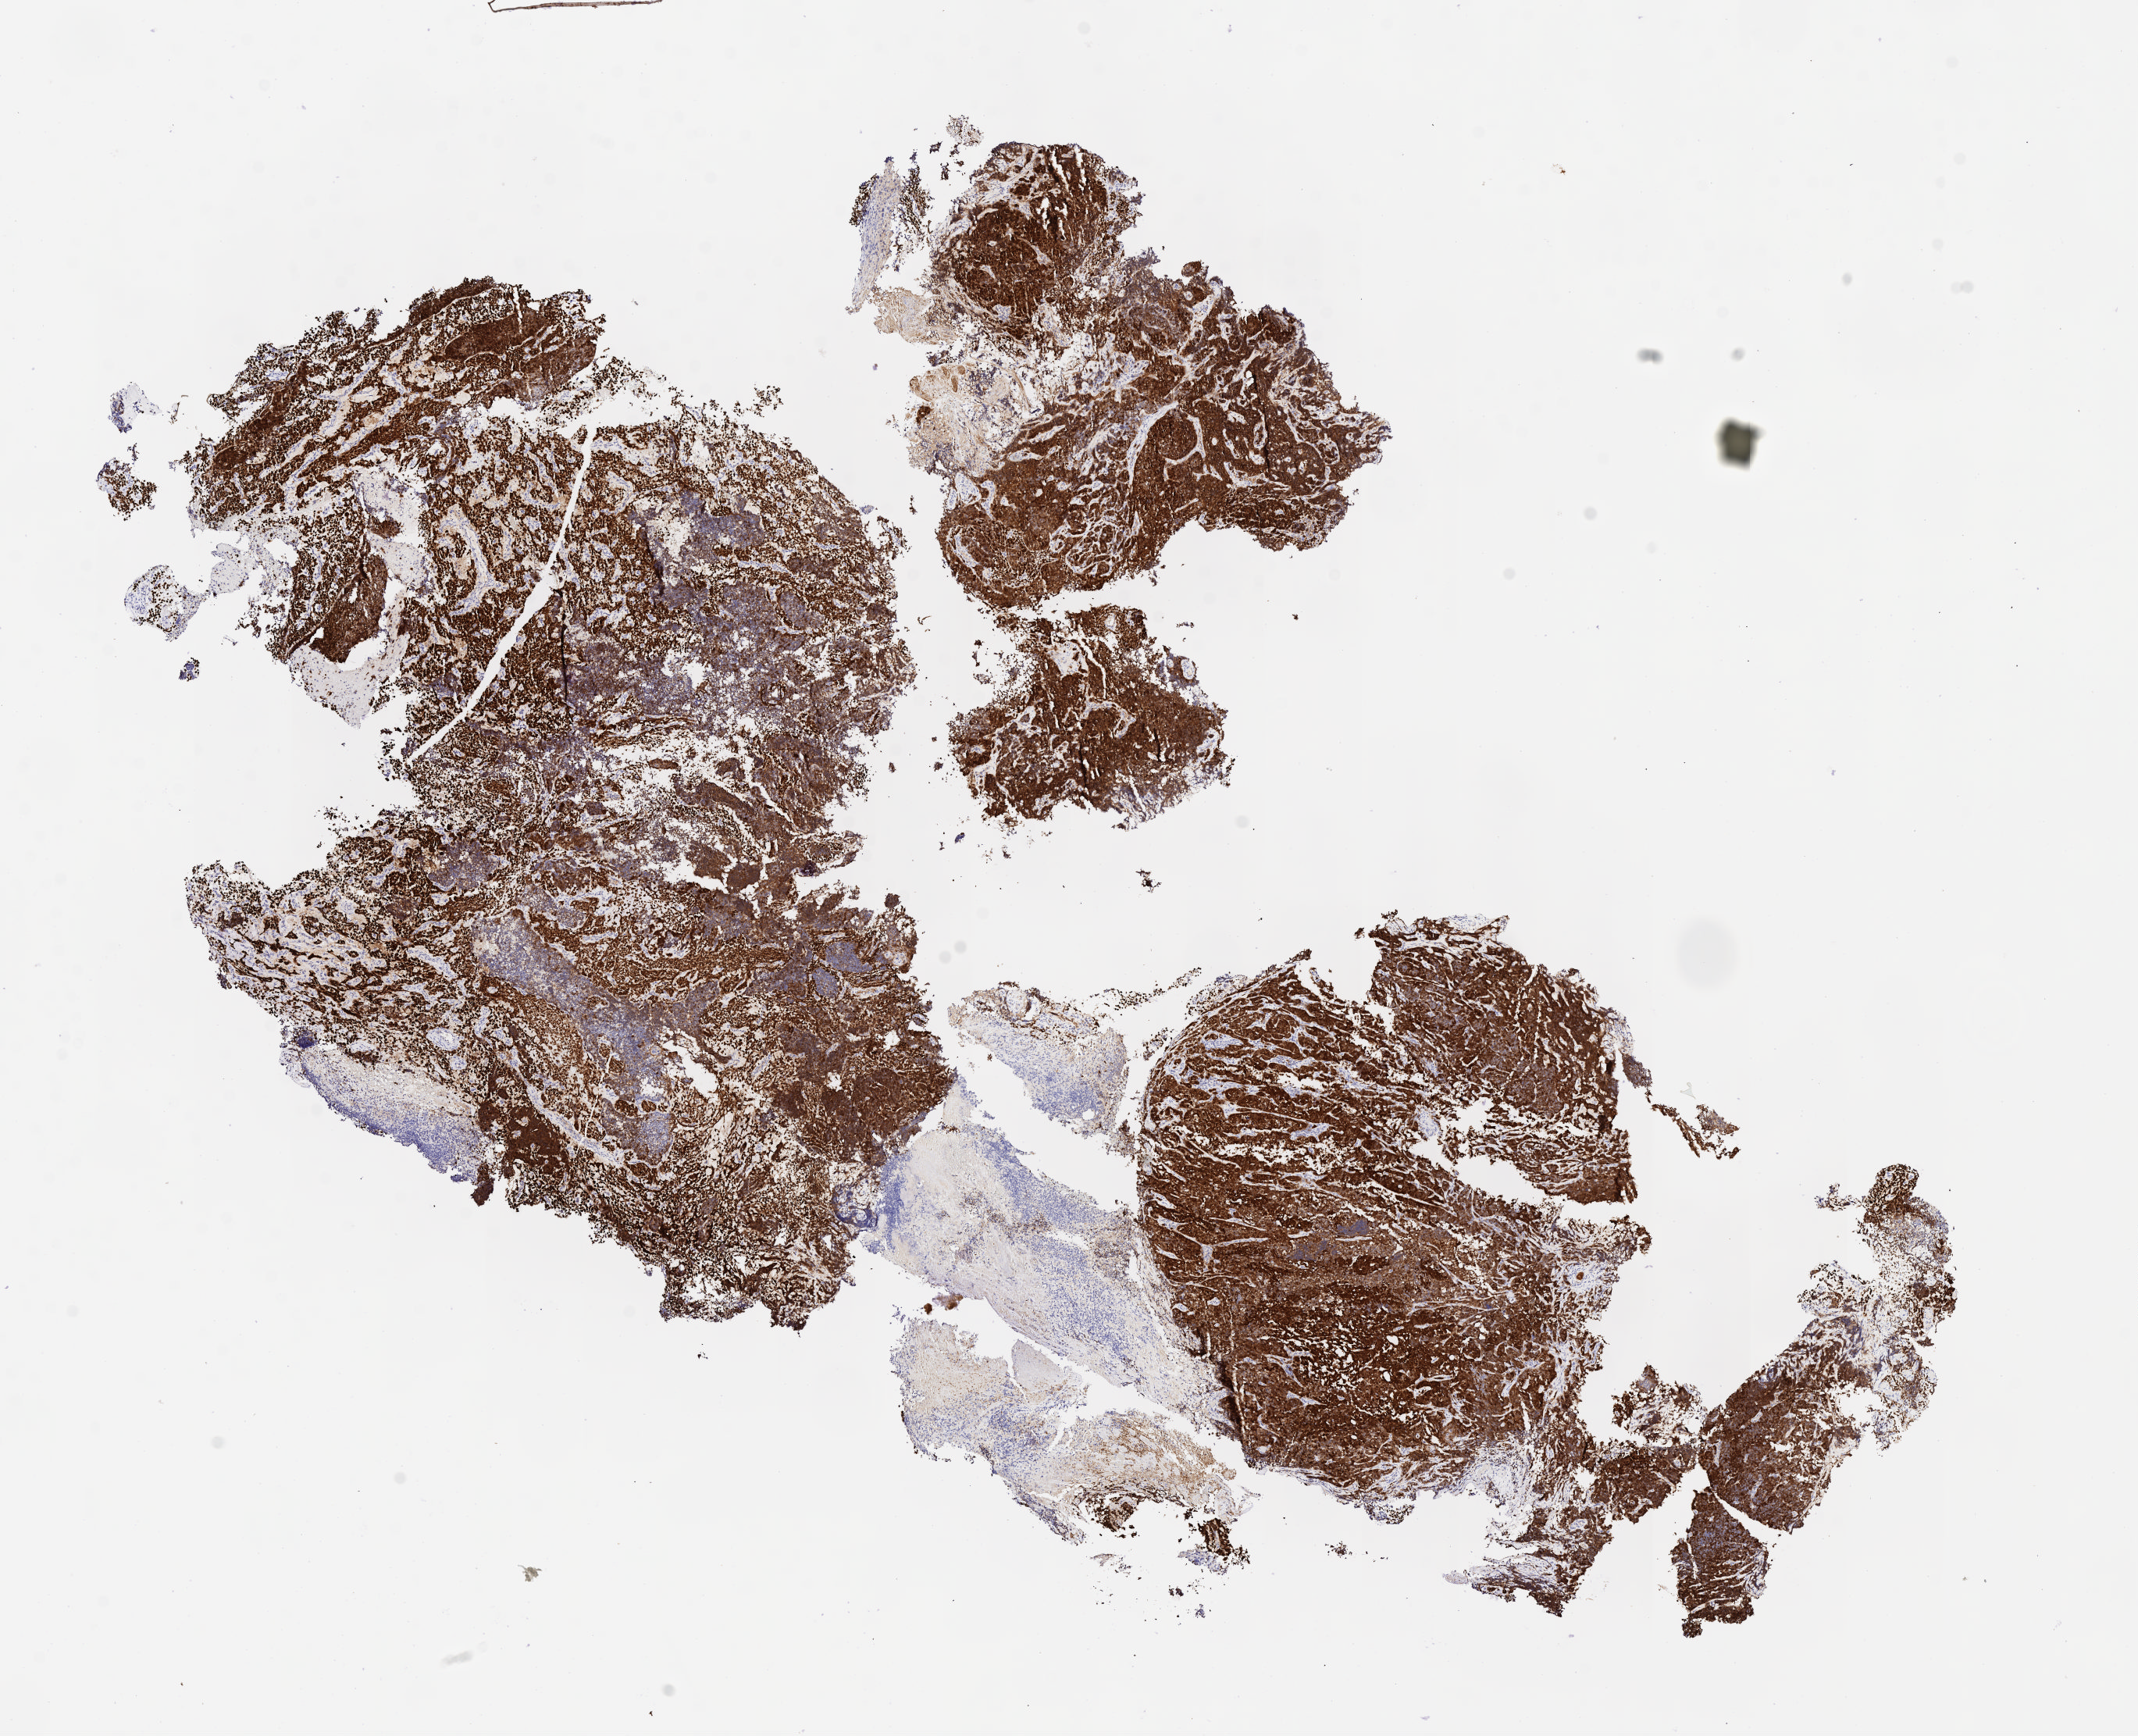
Whole-slide image, immunohistochemical stain for p16 (p16INK4a), a low-resolution overview of the entire scanned area, about 11.1 x 9.0 mm; specimen: tumor tissue; anatomic site: cervix. Patient: female, 57 years old.
Diagnosis: Adenosquamous carcinoma.